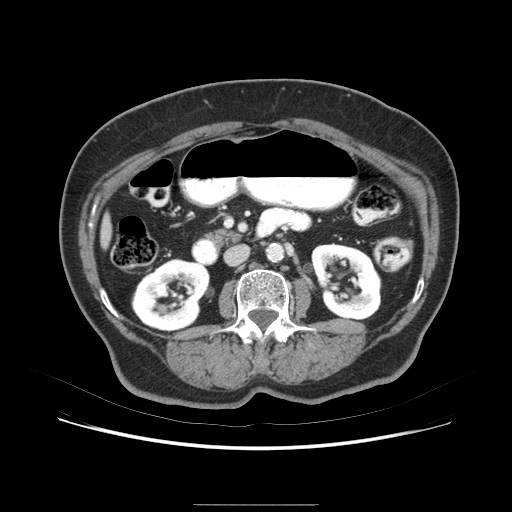
Contrast-enhanced abdominal CT (liver protocol), one axial slice. Slice 20 of 79 in the series (ordered by position). Soft-tissue window (W 400 / L 40 HU). 2.5 mm slice thickness. 512 × 512 image matrix, field of view 380 × 380 mm. From the clinical record (not read from this slice): diagnosis: hepatocellular carcinoma (patient treated with transarterial chemoembolisation; whether this scan precedes or follows treatment is not stated here); TNM stage (as recorded): Stage-I; Child-Pugh class: A.
Structures marked on this image (semi-automatically segmented with operator editing):
- liver parenchyma outside the tumour (the mass and vessels are separate outlines, so this box may not span the whole liver): bounding box <98,198,126,268> (left, top, right, bottom; pixels)